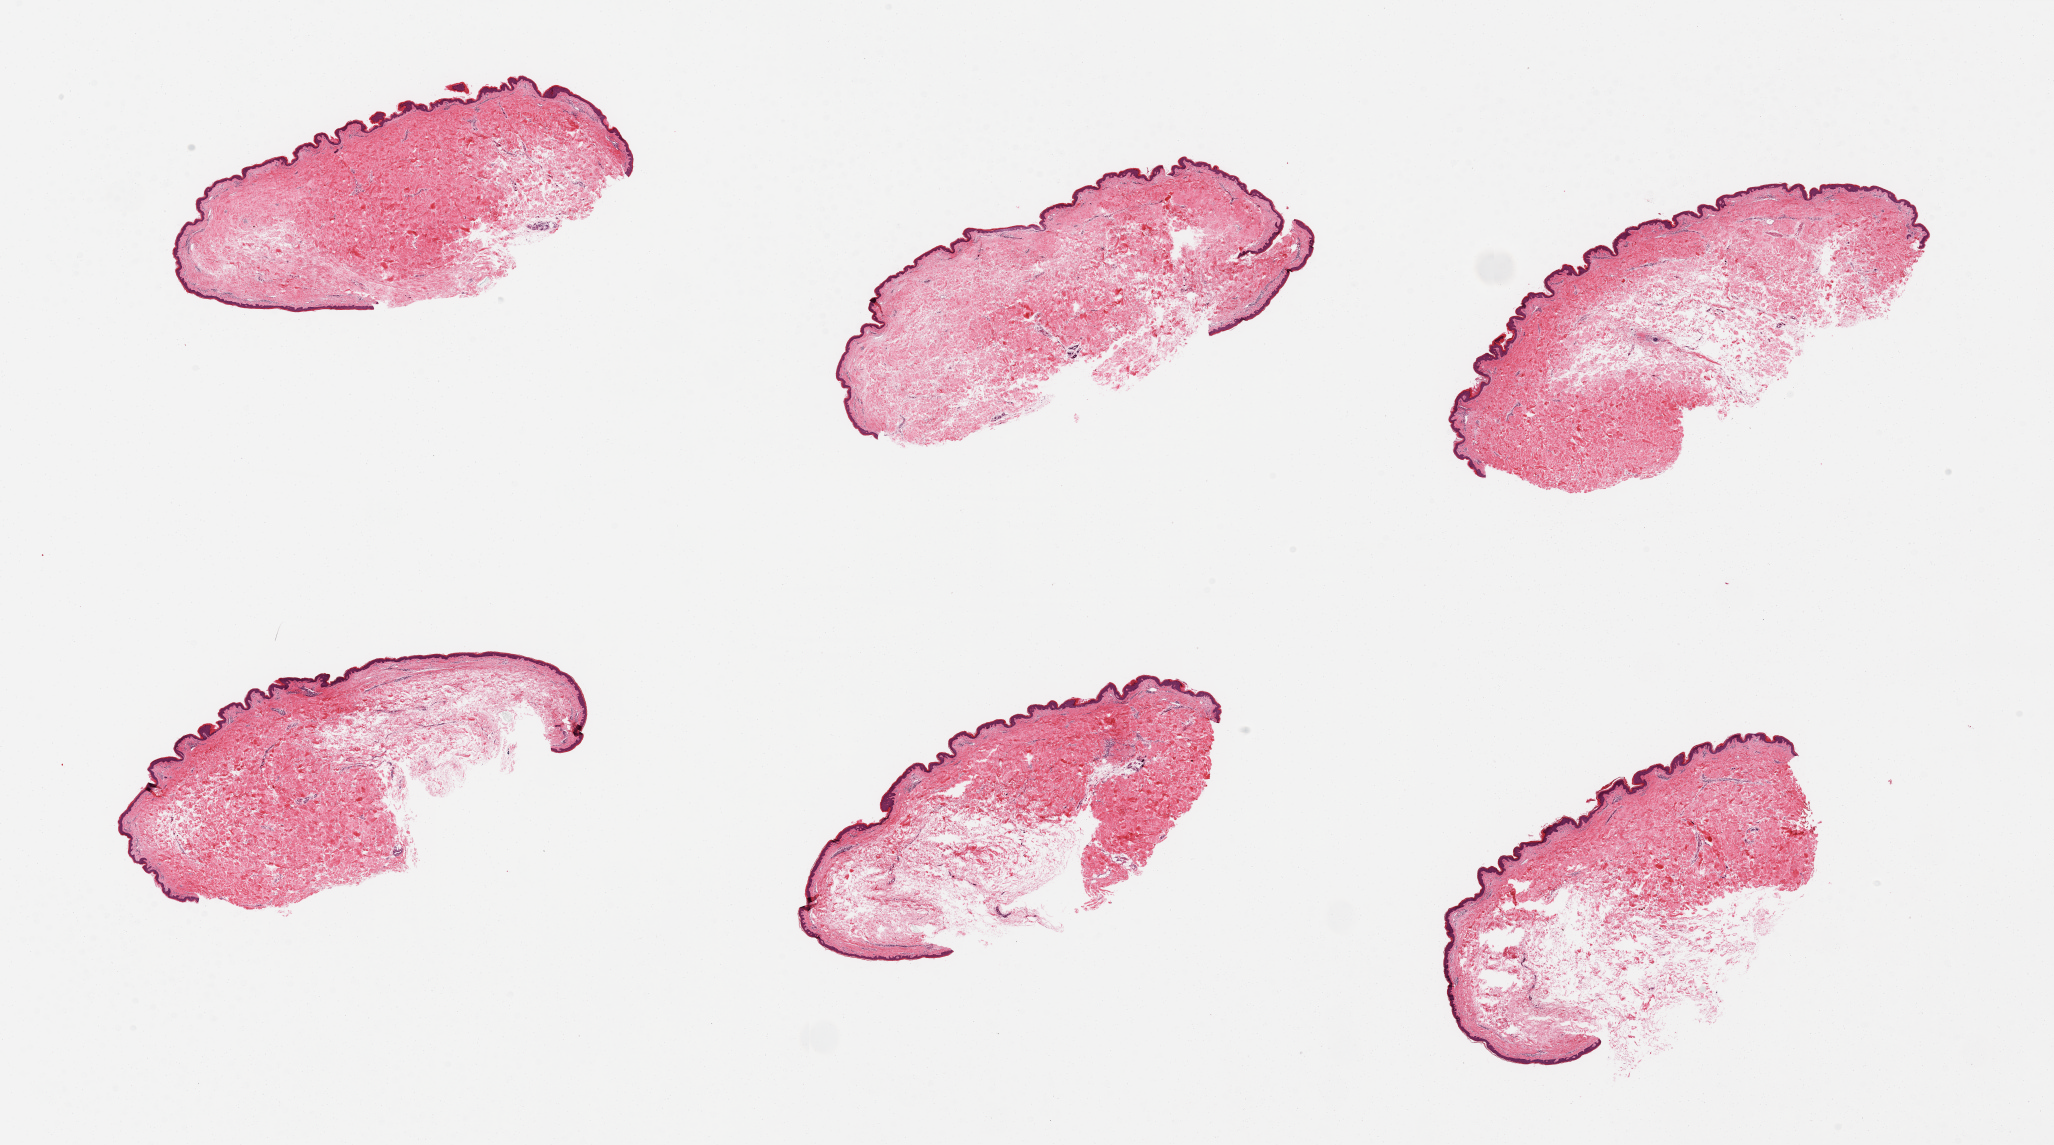
Digitized haematoxylin and eosin-stained section — whole scanned area (about 32.5 x 18.1 mm) shown as a low-resolution overview. PAXgene-fixed paraffin-embedded (PFPE) section. Target tissue: skin of suprapubic region. Tissue donor sample. Donor: female.
- pathologist's review note for this sample: 6 pieces, well trimmed